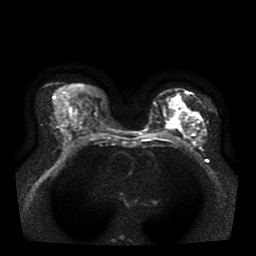
Breast MRI, one axial slice. Slice 22 of 39 in the series (ordered by position). Diffusion-weighted series; image 2 of 4 stored at this slice position (different b-values; order by instance number). 1.5 T. 5 mm slice thickness. 256 × 256 image matrix, field of view 330 × 330 mm. Female patient.
Structures marked on this image (manually delineated by an expert):
- tumour on diffusion-weighted imaging: bounding box <167,105,191,128> (left, top, right, bottom; pixels)